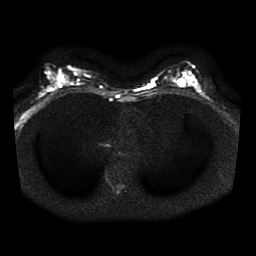
Breast MRI, one axial slice. Slice 19 of 41 in the series (ordered by position). Diffusion-weighted series; image 2 of 4 stored at this slice position (different b-values; order by instance number). 1.5 T. 256 × 256 image matrix. Female patient.
Annotated regions visible in this slice (outlined manually by an expert reader):
- tumour on diffusion-weighted imaging: bounding box [x1, y1, x2, y2] px = [185, 76, 196, 88]